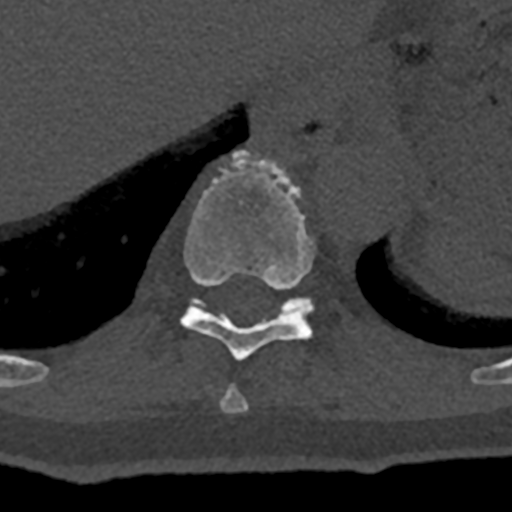
CT including the spine, one axial slice; position 596 of 797 along the scan axis; reconstruction kernel Br40s/3; bone window (W 1800 / L 400 HU); 512 × 512 image matrix, field of view 160 × 160 mm. Male patient, age 74 years. From the clinical record (not read from this slice): primary cancer: renal.
Outlined on this slice (semi-automatically segmented with operator editing):
- T10 vertebra: bounding box [x1, y1, x2, y2] px = [180, 150, 315, 361]
- T11 vertebra: [191, 296, 313, 314]
- T9 vertebra: [220, 386, 249, 413]